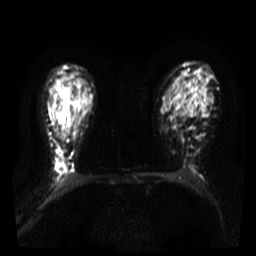
Breast MRI, one axial slice; slice 25 of 36 in the series (ordered by position); diffusion-weighted series; image 2 of 4 stored at this slice position (different b-values; order by instance number); 3 T; 5 mm slice thickness; 256 × 256 image matrix, field of view 300 × 300 mm. Female patient.
Annotated regions visible in this slice (manually delineated by an expert):
- tumour on diffusion-weighted imaging: bounding box (x1, y1, x2, y2) in pixels: (57, 152, 67, 173)